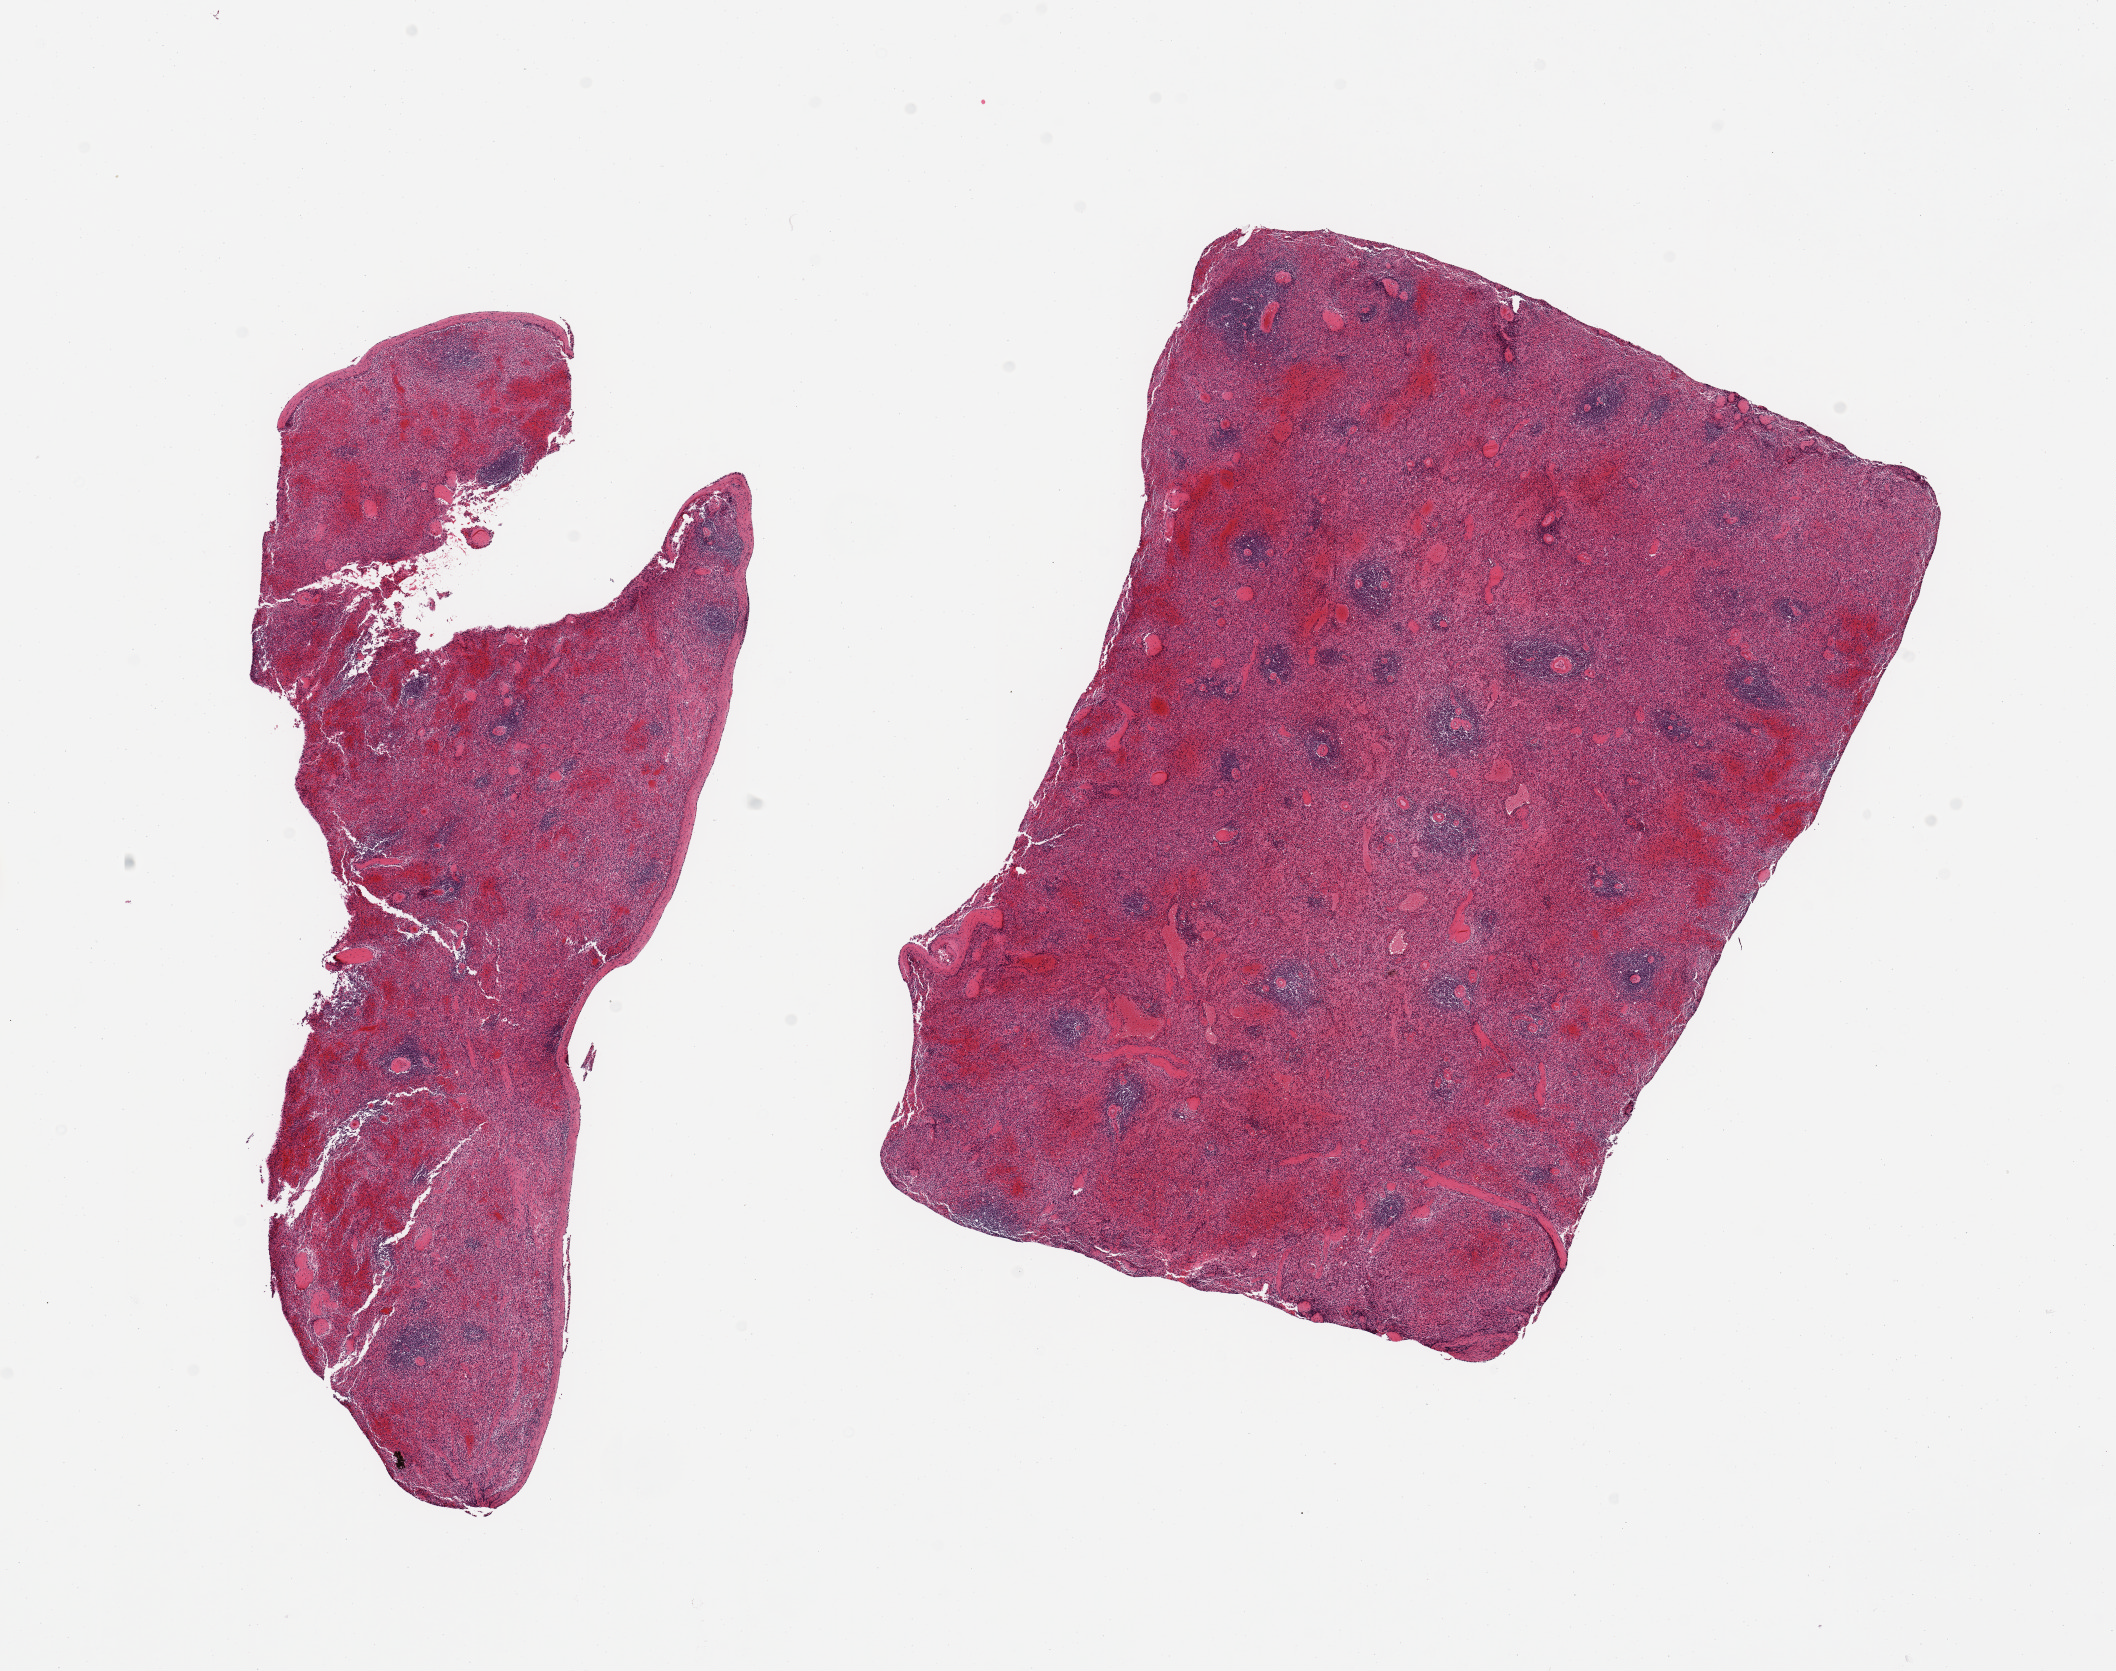
Digitized hematoxylin and eosin (H&E)-stained section, low-resolution overview of the scanned area, about 16.7 x 13.2 mm (acquisition: 20x scan). PAXgene-fixed paraffin-embedded (PFPE) section. Sampled site (target tissue): spleen. Tissue donor sample. Male donor.
Pathologist's review note for this sample: 2 pieces; moderately congested; capsule present.